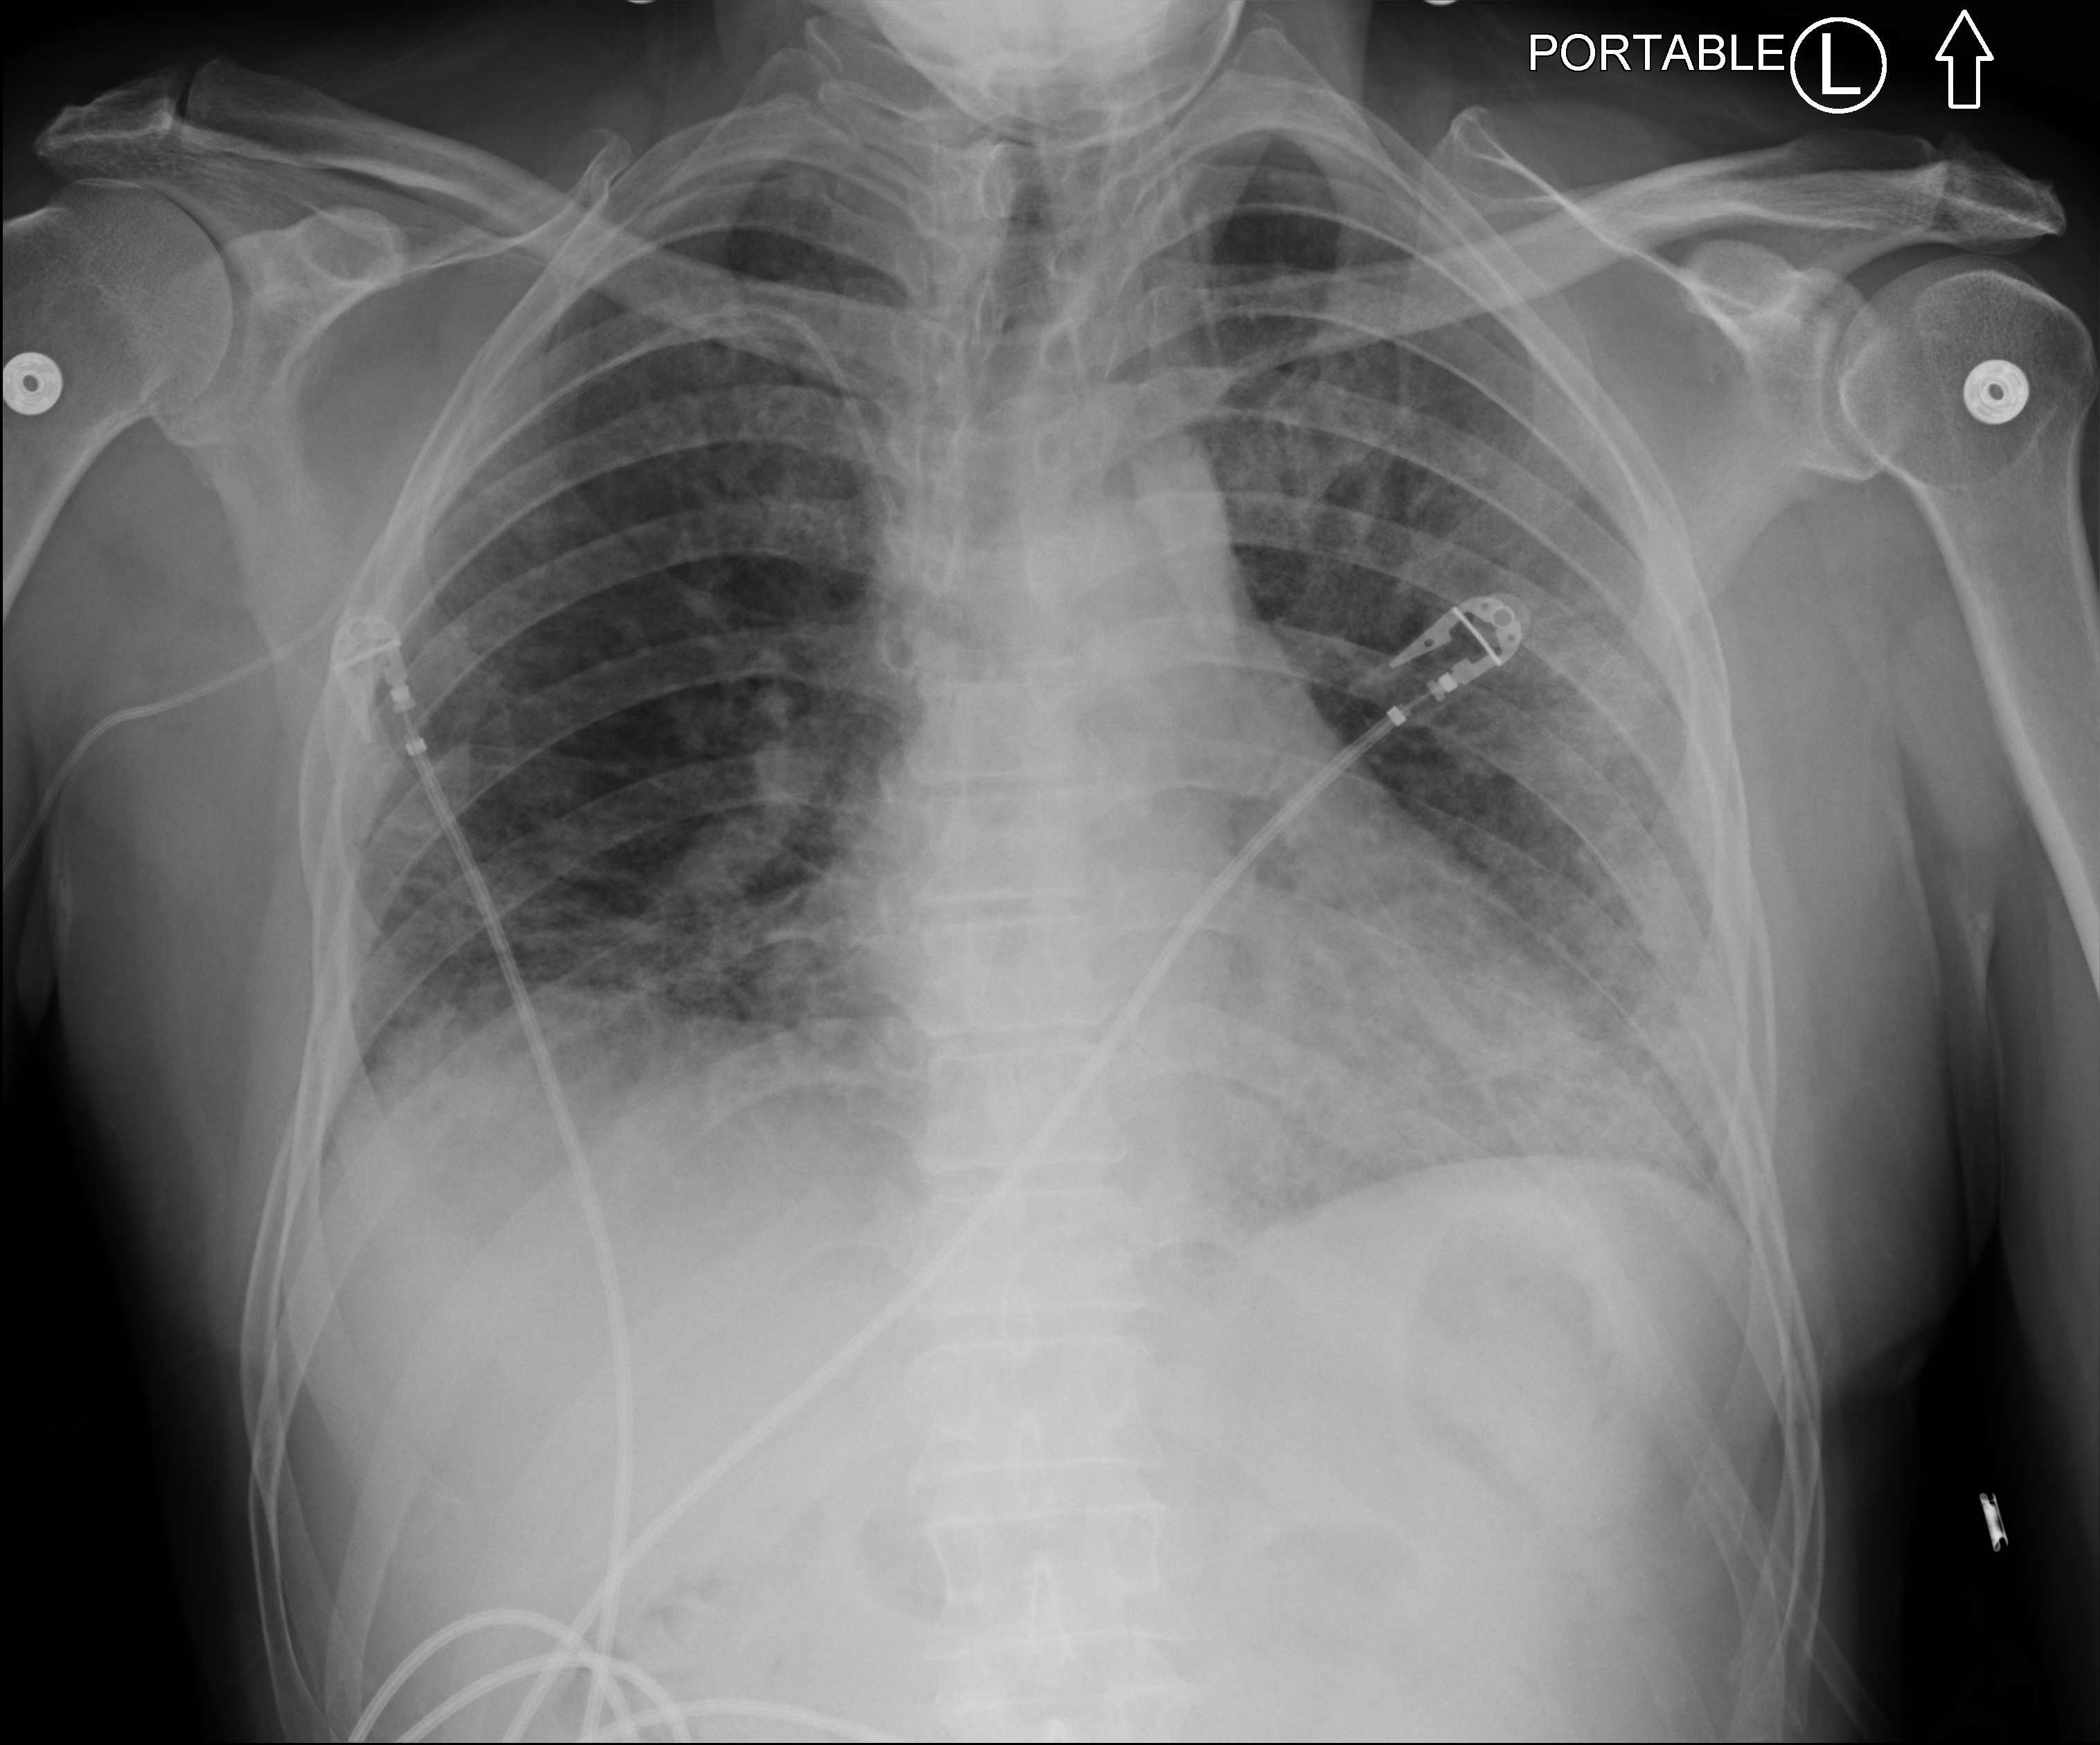
Bedside chest radiograph (computed radiography). Male patient hospitalised with COVID-19, age 18–59 years.
From the hospital-stay record, not from the radiograph (when in the stay this image was taken is not recorded): admitted to intensive care during this hospital stay: yes.